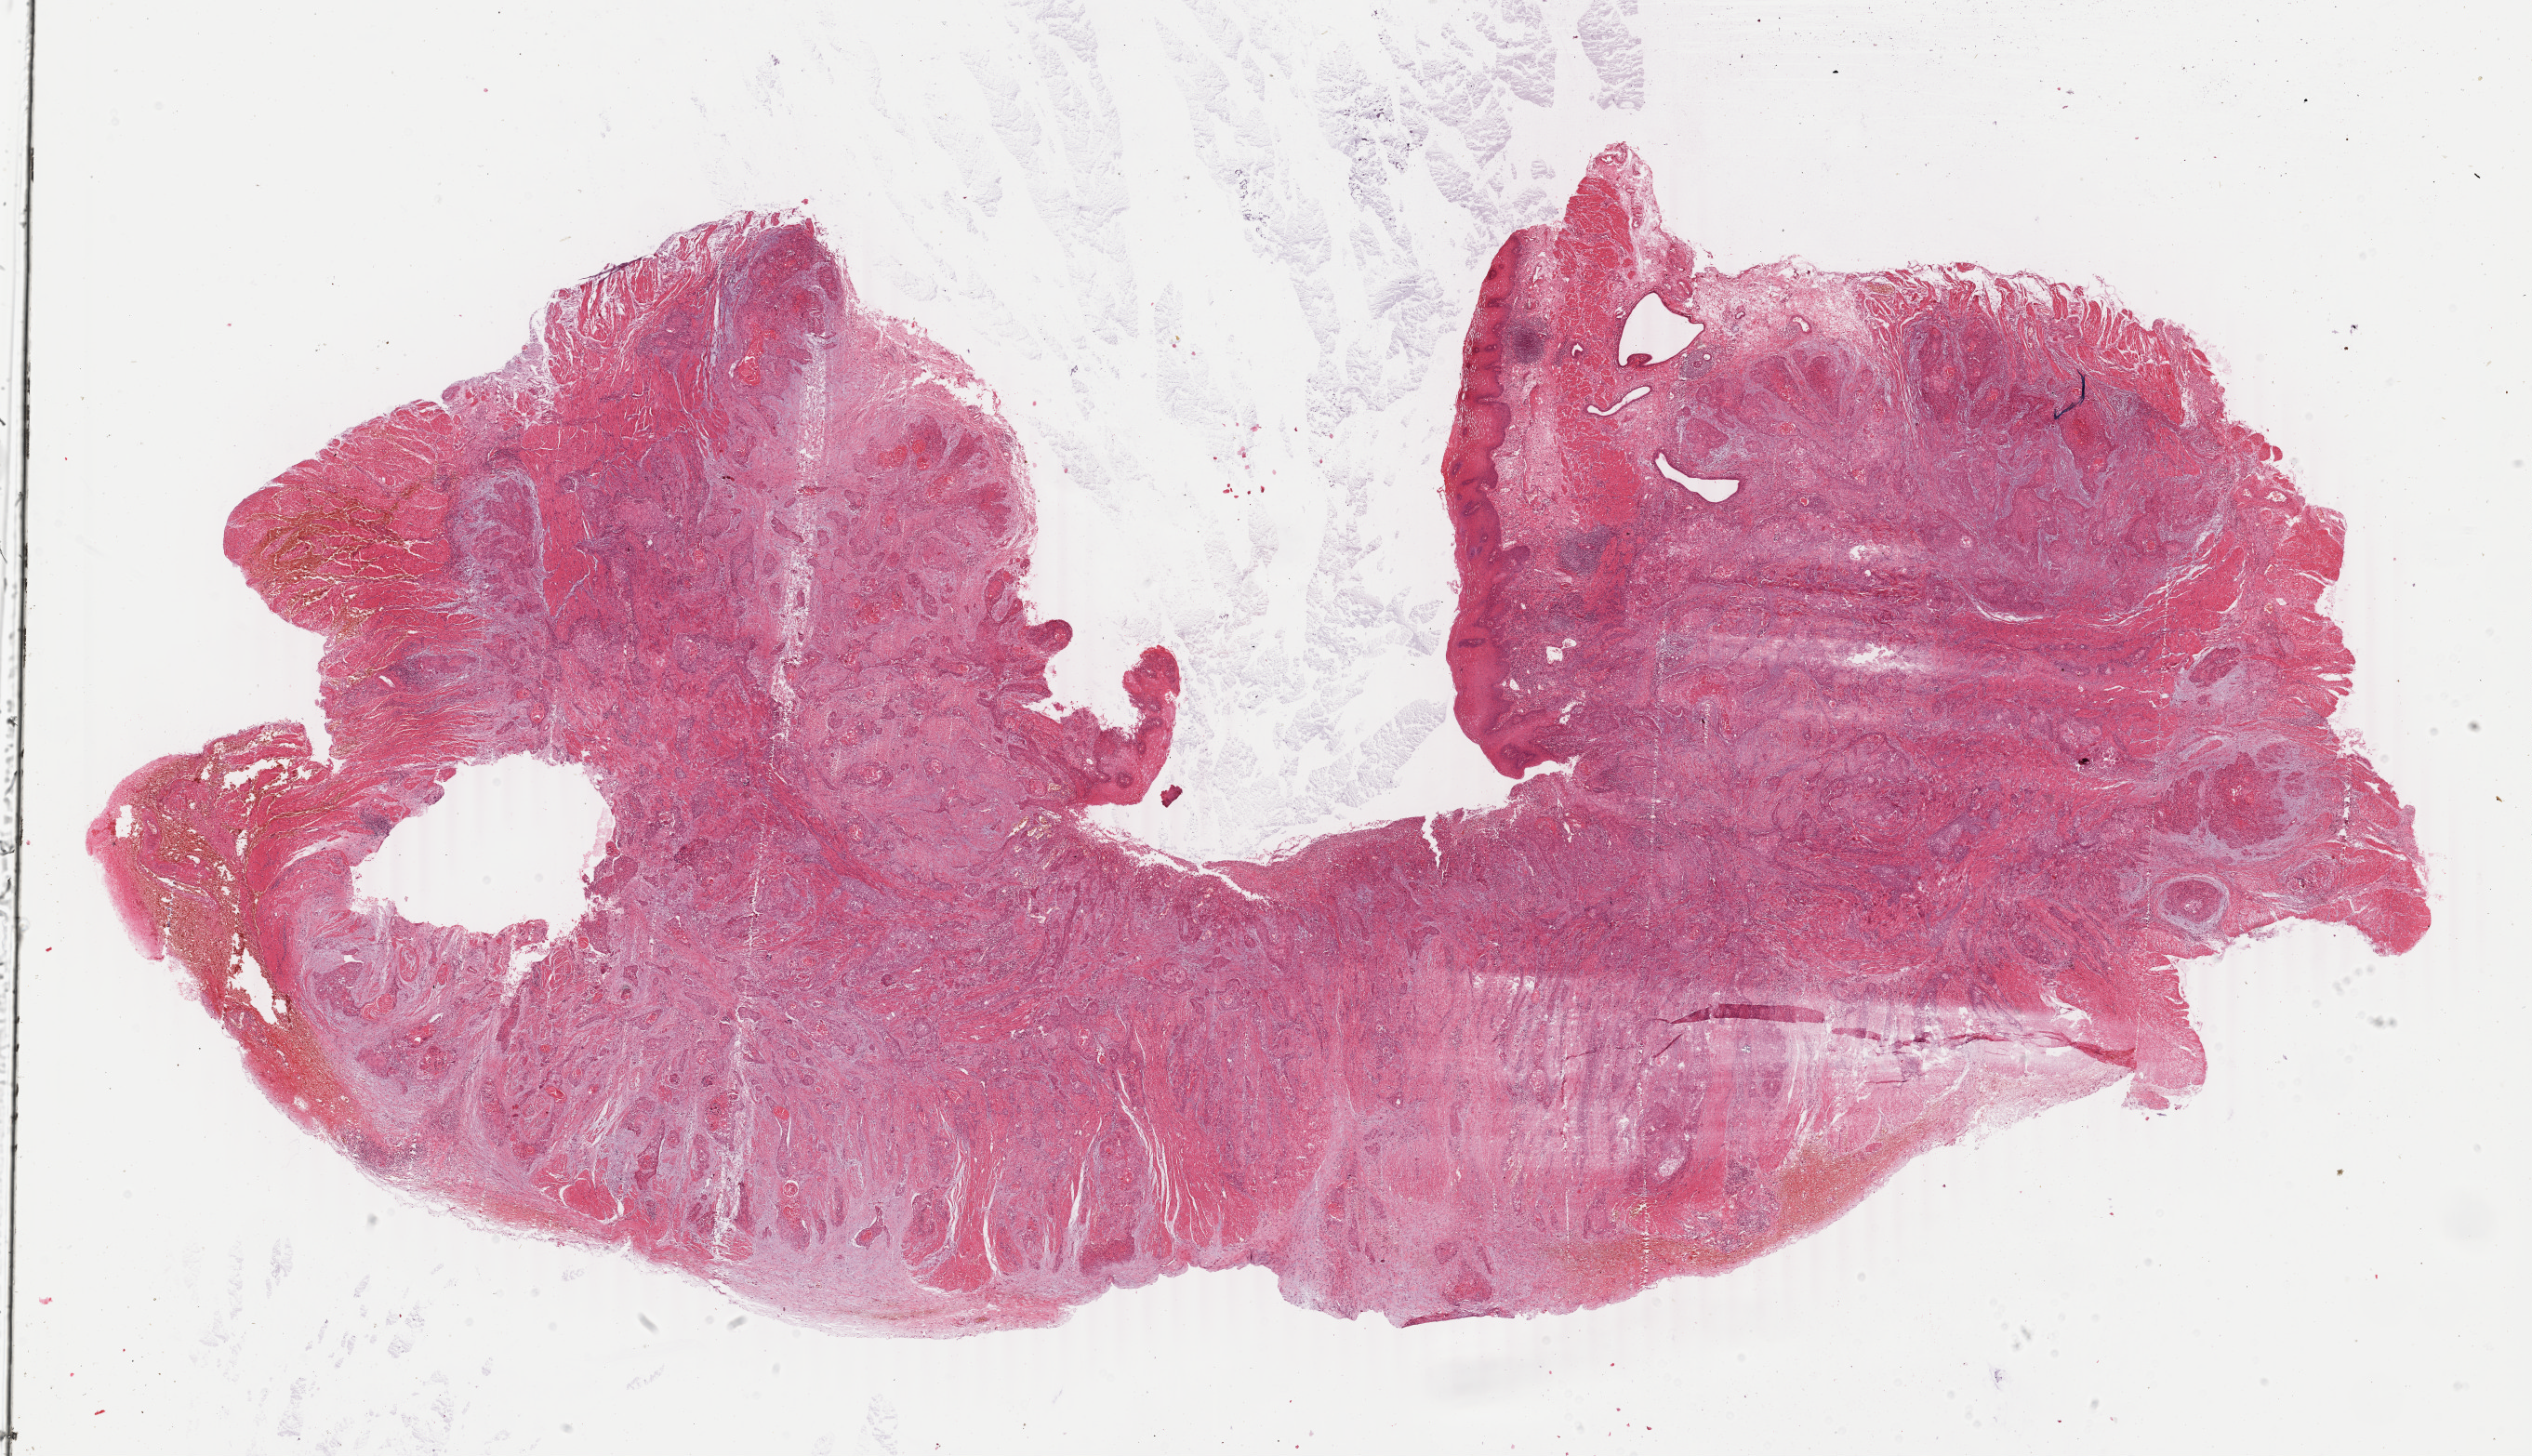
Whole-slide histology image, H&E — shown as a low-resolution overview of the whole scanned area (about 21.7 x 12.5 mm). FFPE section. Primary tumour sample from the esophagus. Male patient; age at initial diagnosis 50 years. Histologic grade: G2 (moderately differentiated).
AJCC pathologic stage: IIB (6th edition). Lymph nodes positive (case pathology): 1 of 4 examined. Pathologic diagnosis: Squamous cell carcinoma, NOS (middle third of esophagus).